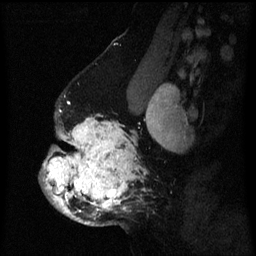
Breast MRI (dynamic contrast-enhanced), one sagittal slice; slice 42 of 60 in the series (ordered by position); dynamic contrast-enhanced series, image 2 of 3 at this slice position (ordered by acquisition); 1.5 T; TE 4.2 ms, TR 8 ms; 256 × 256 image matrix. Patient: female, 50 years.
Structures marked on this image (semi-automatic segmentation, software-assisted and operator-edited):
- analysis volume of interest (the breast-tissue region the enhancement analysis was run in; not a lesion): bounding box <39,105,138,226> (left, top, right, bottom; pixels)
- tumour enhancement mask (voxels above the 70 % enhancement threshold inside the analysis volume of interest): <43,118,138,224>